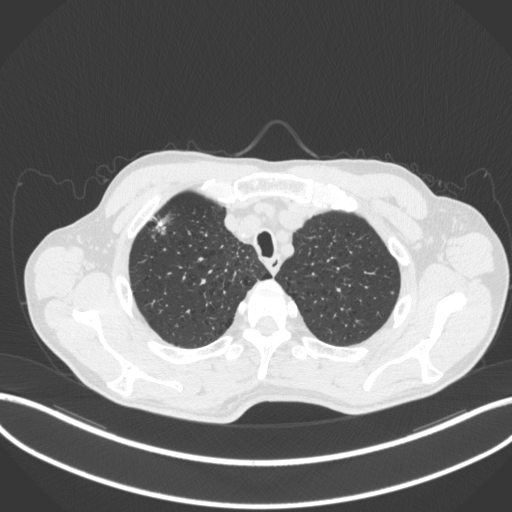
Chest CT, one axial slice; position 361 of 414 along the scan axis; reconstruction kernel B31f; 120 kVp; lung window (W 1500 / L -600 HU); 1 mm slice thickness; 512 × 512 image matrix. Male patient, age 69 years. Case-level facts recorded for this patient, not image findings: clinical TNM (as recorded): T1b N1 M0.
Structures marked on this image (bounding box drawn by a radiologist):
- lung tumour (recorded histology: adenocarcinoma): bounding box <152,211,173,239> (left, top, right, bottom; pixels)